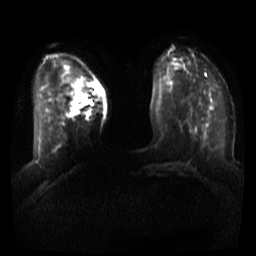
Breast MRI, one axial slice; position 12 of 44 along the scan axis; diffusion-weighted series; image 2 of 4 stored at this slice position (different b-values; order by instance number); 3 T; 256 × 256 image matrix. Female patient.
Structures marked on this image (expert manual segmentation):
- tumour on diffusion-weighted imaging: bounding box <73,94,87,115> (left, top, right, bottom; pixels)